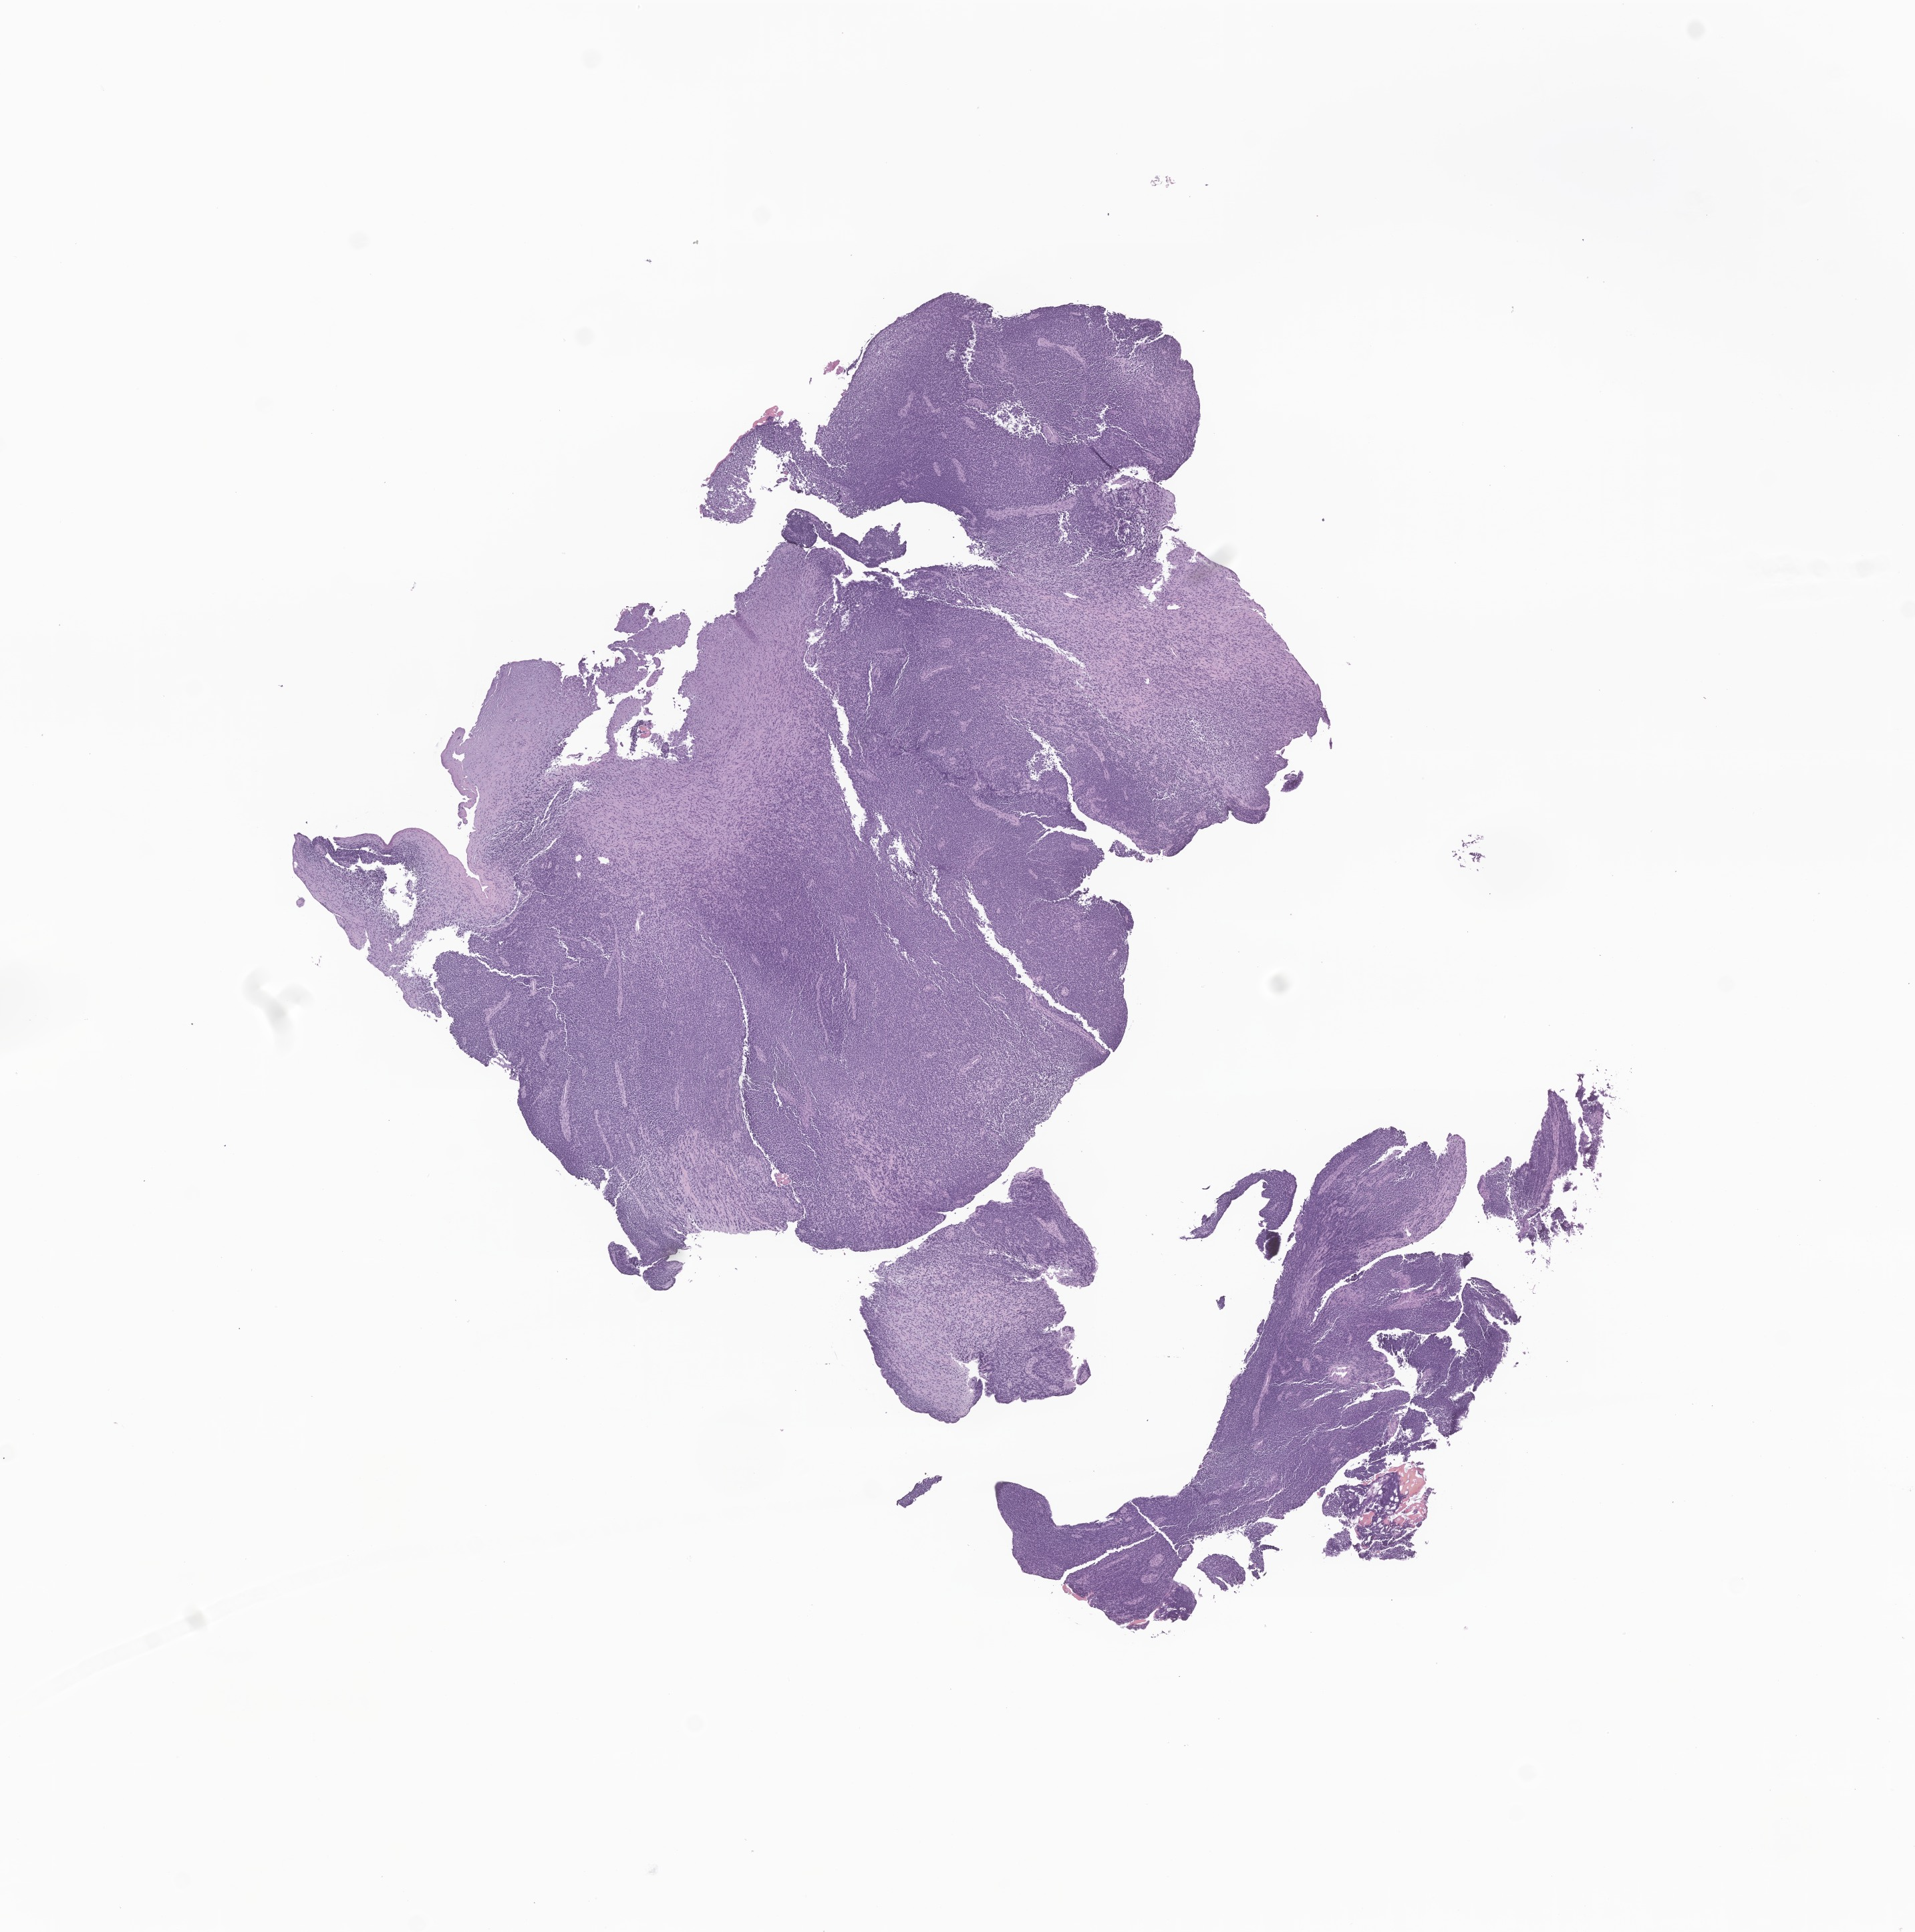
Digitized haematoxylin and eosin-stained section of tumor tissue from the upper limb — shown as a low-resolution overview of the whole scanned area (about 12.1 x 12.2 mm); formalin-fixed paraffin-embedded section. Male patient, age 70 days.
* diagnosis (ICD-O-3 morphology term): Alveolar rhabdomyosarcoma